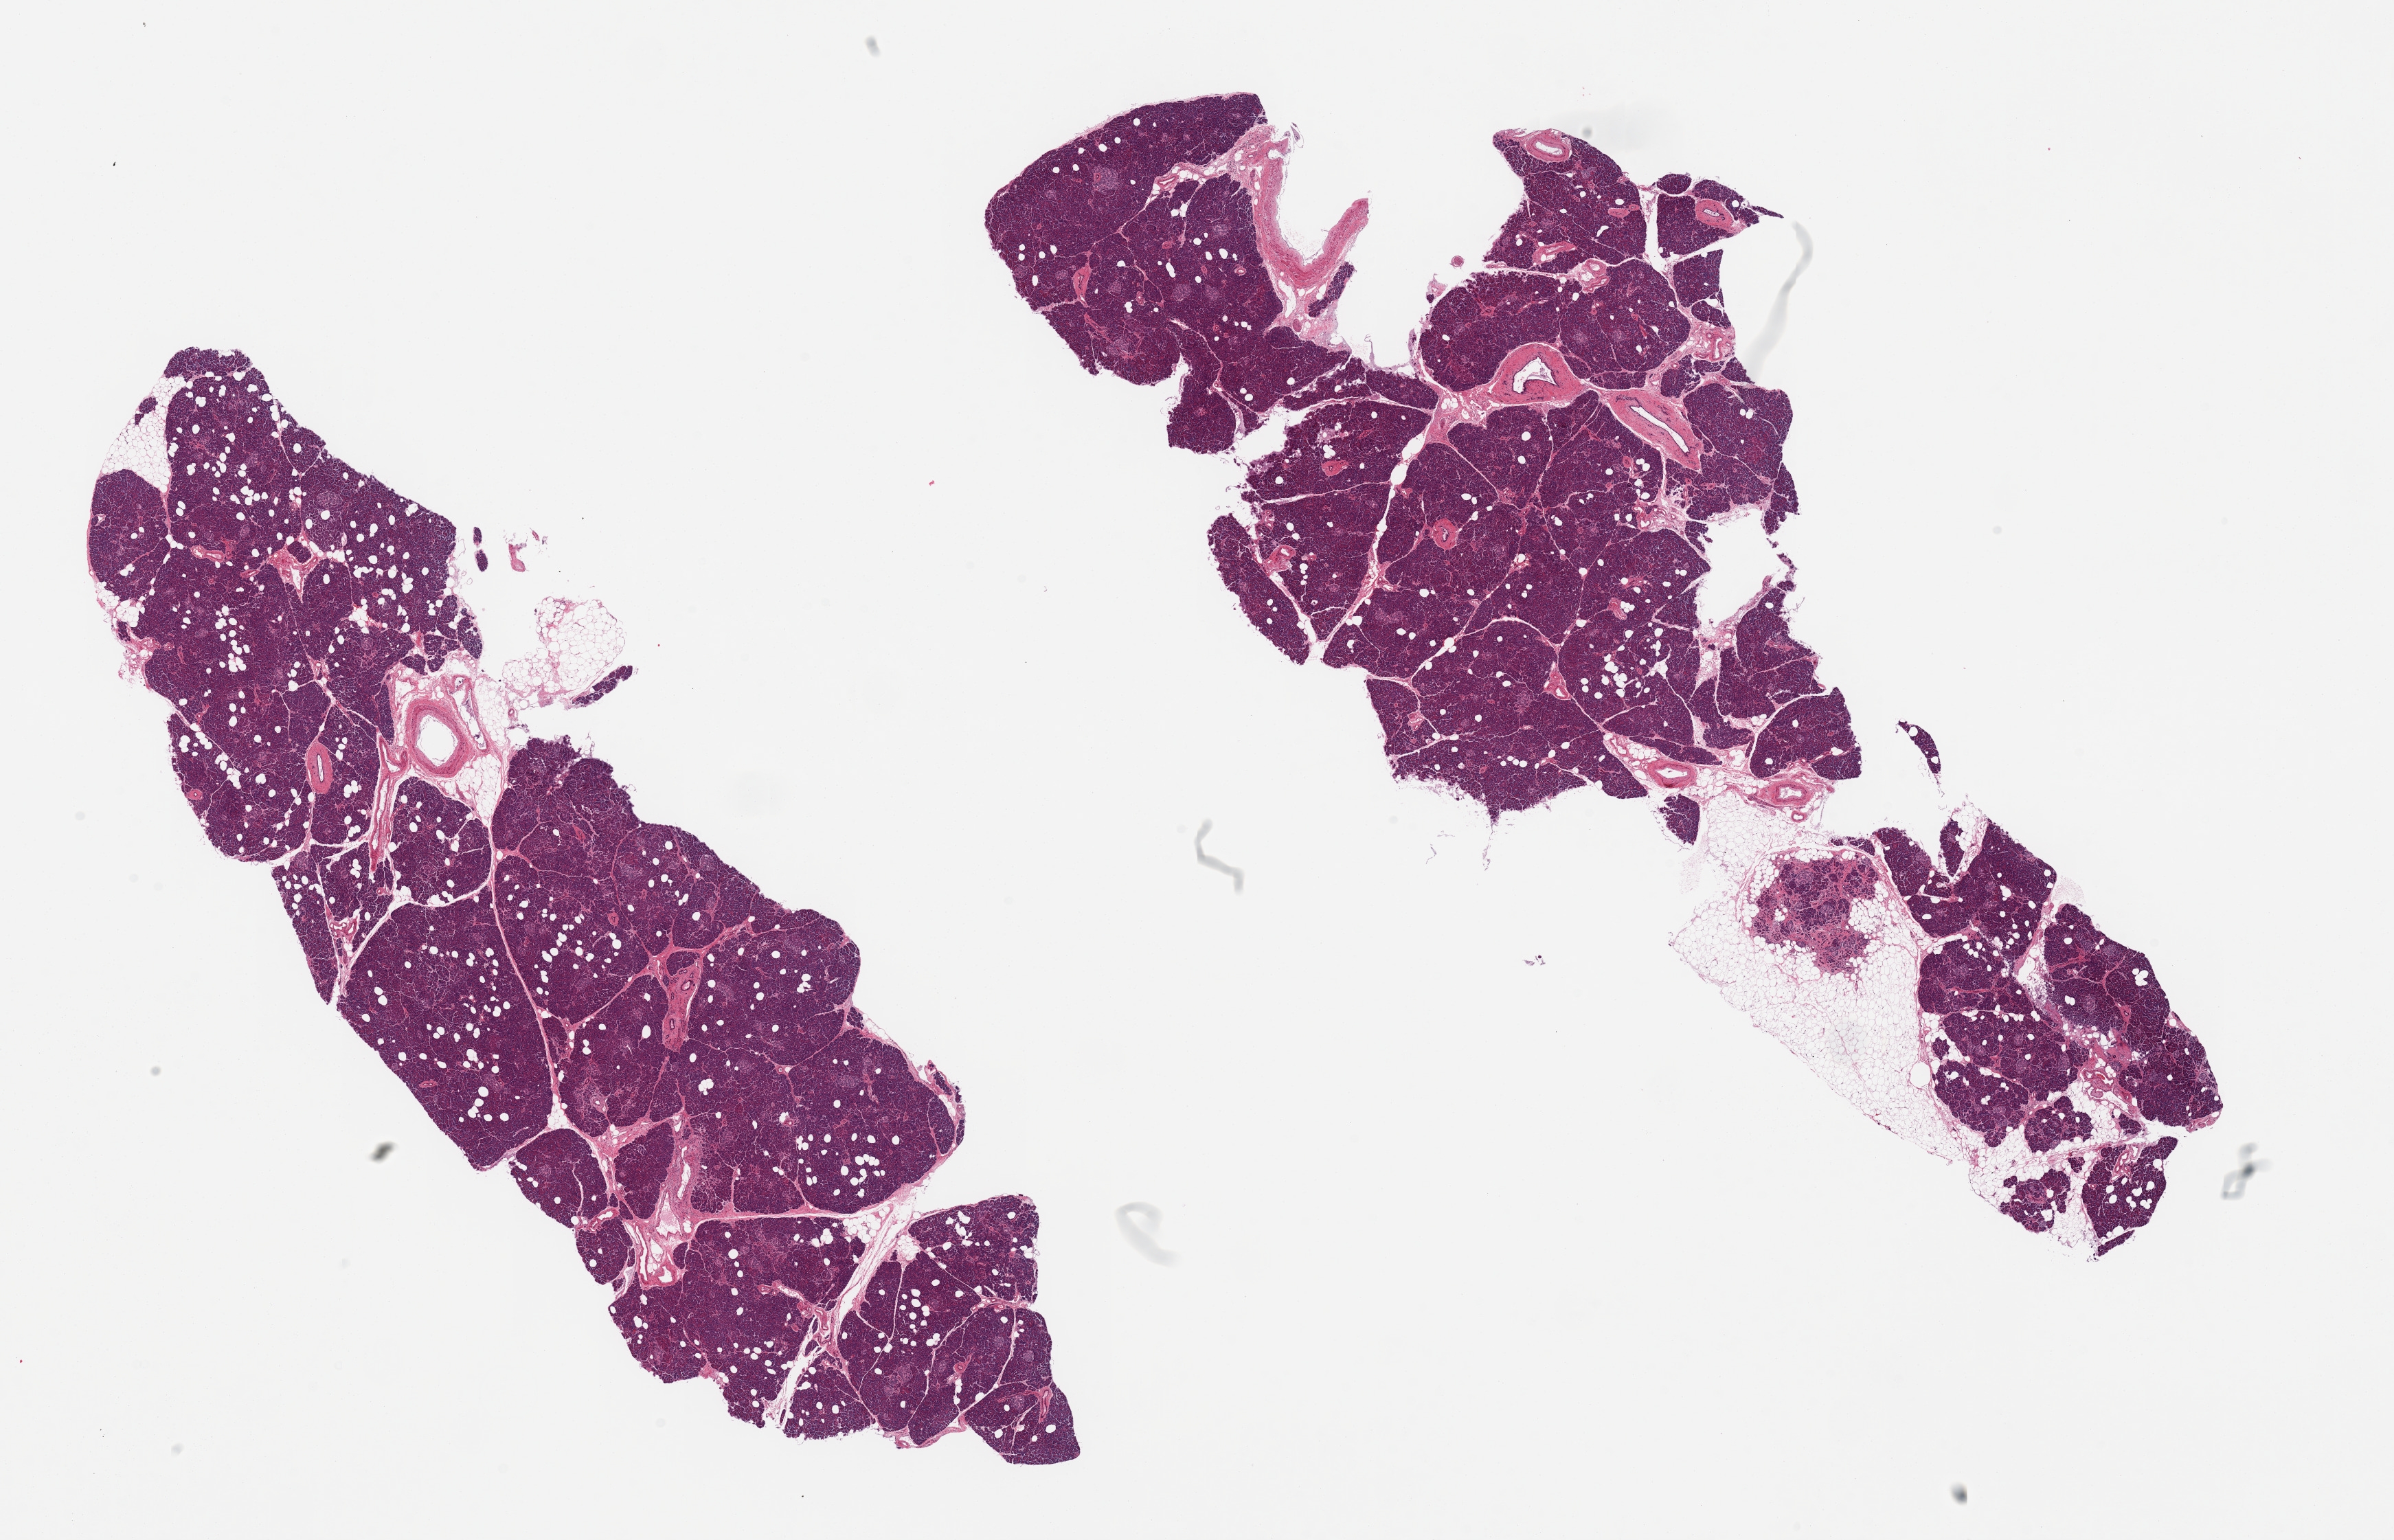
Whole-slide image, haematoxylin and eosin stain, brightfield, shown as a low-resolution overview of the whole scanned area (about 27.6 x 17.7 mm), PAXgene-fixed, paraffin-embedded tissue, section of pancreas (target tissue), donor tissue sample. Donor sex: female.
Reviewer comment on this tissue sample: 2 pieces, well-preserved; Islets well visualized; ? Small hamartoma.